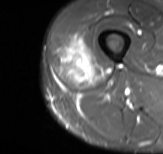
MRI of an extremity soft-tissue mass, one axial slice; position 22 of 61 along the scan axis; STIR; MR volume resampled by the dataset authors to the PET/CT grid (not the native acquisition matrix); 3.27 mm slice thickness; 163 × 154 image matrix, field of view 159 × 150 mm. Male patient. Case-level facts recorded for this patient, not image findings: histological type: poorly differentiated synovial sarcoma; grade: high; site of the primary tumour: right buttock.
Outlined on this slice (expert contour drawn on MRI and transferred to this co-registered scan by the dataset authors):
- gross tumour volume including surrounding oedema: bounding box [x1, y1, x2, y2] px = [59, 36, 104, 88]